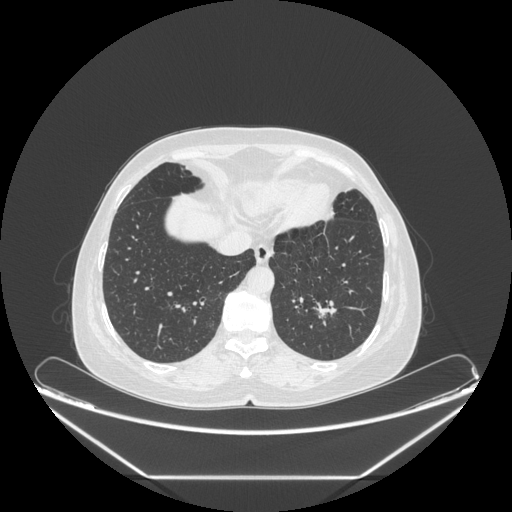
Chest CT, one axial slice. Position 67 of 241 along the scan axis. Lung window (W 1500 / L -600 HU). 512 × 512 image matrix. Female patient, age 63 years. Case-level facts recorded for this patient, not image findings: clinical TNM (as recorded): T1c N0 M0; histopathological grade: G2-3.
Annotated regions visible in this slice (bounding box drawn by a radiologist):
- lung tumour (recorded histology: adenocarcinoma): bounding box (x1, y1, x2, y2) in pixels: (307, 293, 350, 341)